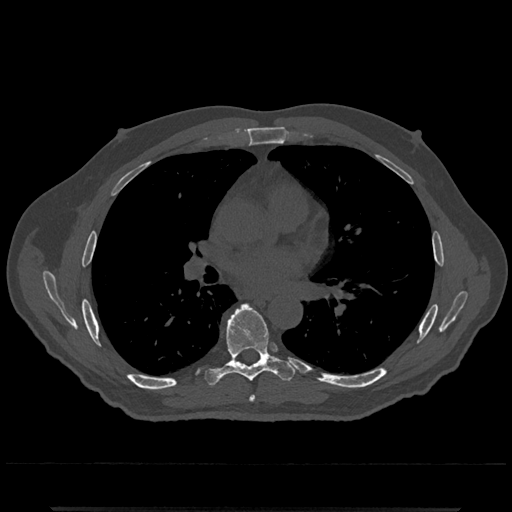
CT including the spine, one axial slice. Reconstruction kernel Br40s/3. Bone window (W 1800 / L 400 HU). 512 × 512 image matrix, field of view 393 × 393 mm. Male patient, age 67 years. From the clinical record (not read from this slice): primary cancer: prostate.
Annotated regions visible in this slice (semi-automatic segmentation, software-assisted and operator-edited):
- T6 vertebra: bounding box (x1, y1, x2, y2) in pixels: (249, 395, 256, 402)
- T7 vertebra: (206, 304, 295, 385)